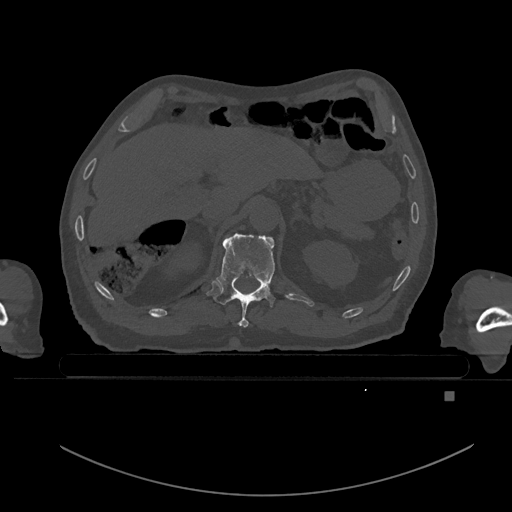
CT including the spine, one axial slice; slice 27 of 969 in the series (ordered by position); bone window (W 1800 / L 400 HU); 0.5 mm slice thickness; 512 × 512 image matrix, field of view 456 × 456 mm. Male patient, age 82 years. Case-level facts recorded for this patient, not image findings: primary cancer: prostate; vertebrae with lytic lesions (as recorded): T11, T9, T8, T2.
Annotated regions visible in this slice (semi-automatically segmented with operator editing):
- T11 vertebra: bounding box [x1, y1, x2, y2] px = [214, 233, 276, 327]